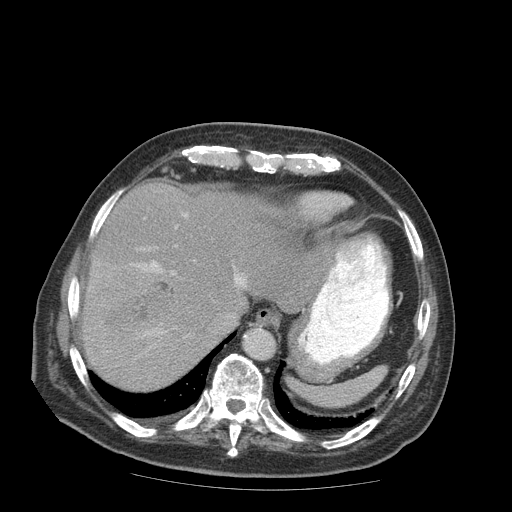
Contrast-enhanced abdominal CT (liver protocol), one axial slice. Position 70 of 99 along the scan axis. Reconstruction kernel STANDARD. Soft-tissue window (W 400 / L 40 HU). 2.5 mm slice thickness. 512 × 512 image matrix. Case-level facts recorded for this patient, not image findings: diagnosis: hepatocellular carcinoma (patient treated with transarterial chemoembolisation; whether this scan precedes or follows treatment is not stated here); TNM stage (as recorded): Stage-IIIB; Child-Pugh class: A; tumour differentiation: well differentiated; tumour nodularity: multinodular.
Structures marked on this image (semi-automatic segmentation, software-assisted and operator-edited):
- liver parenchyma outside the tumour (the mass and vessels are separate outlines, so this box may not span the whole liver): bounding box <82,182,314,390> (left, top, right, bottom; pixels)
- mass: <97,264,179,338>
- liver vessels: <134,214,245,337>